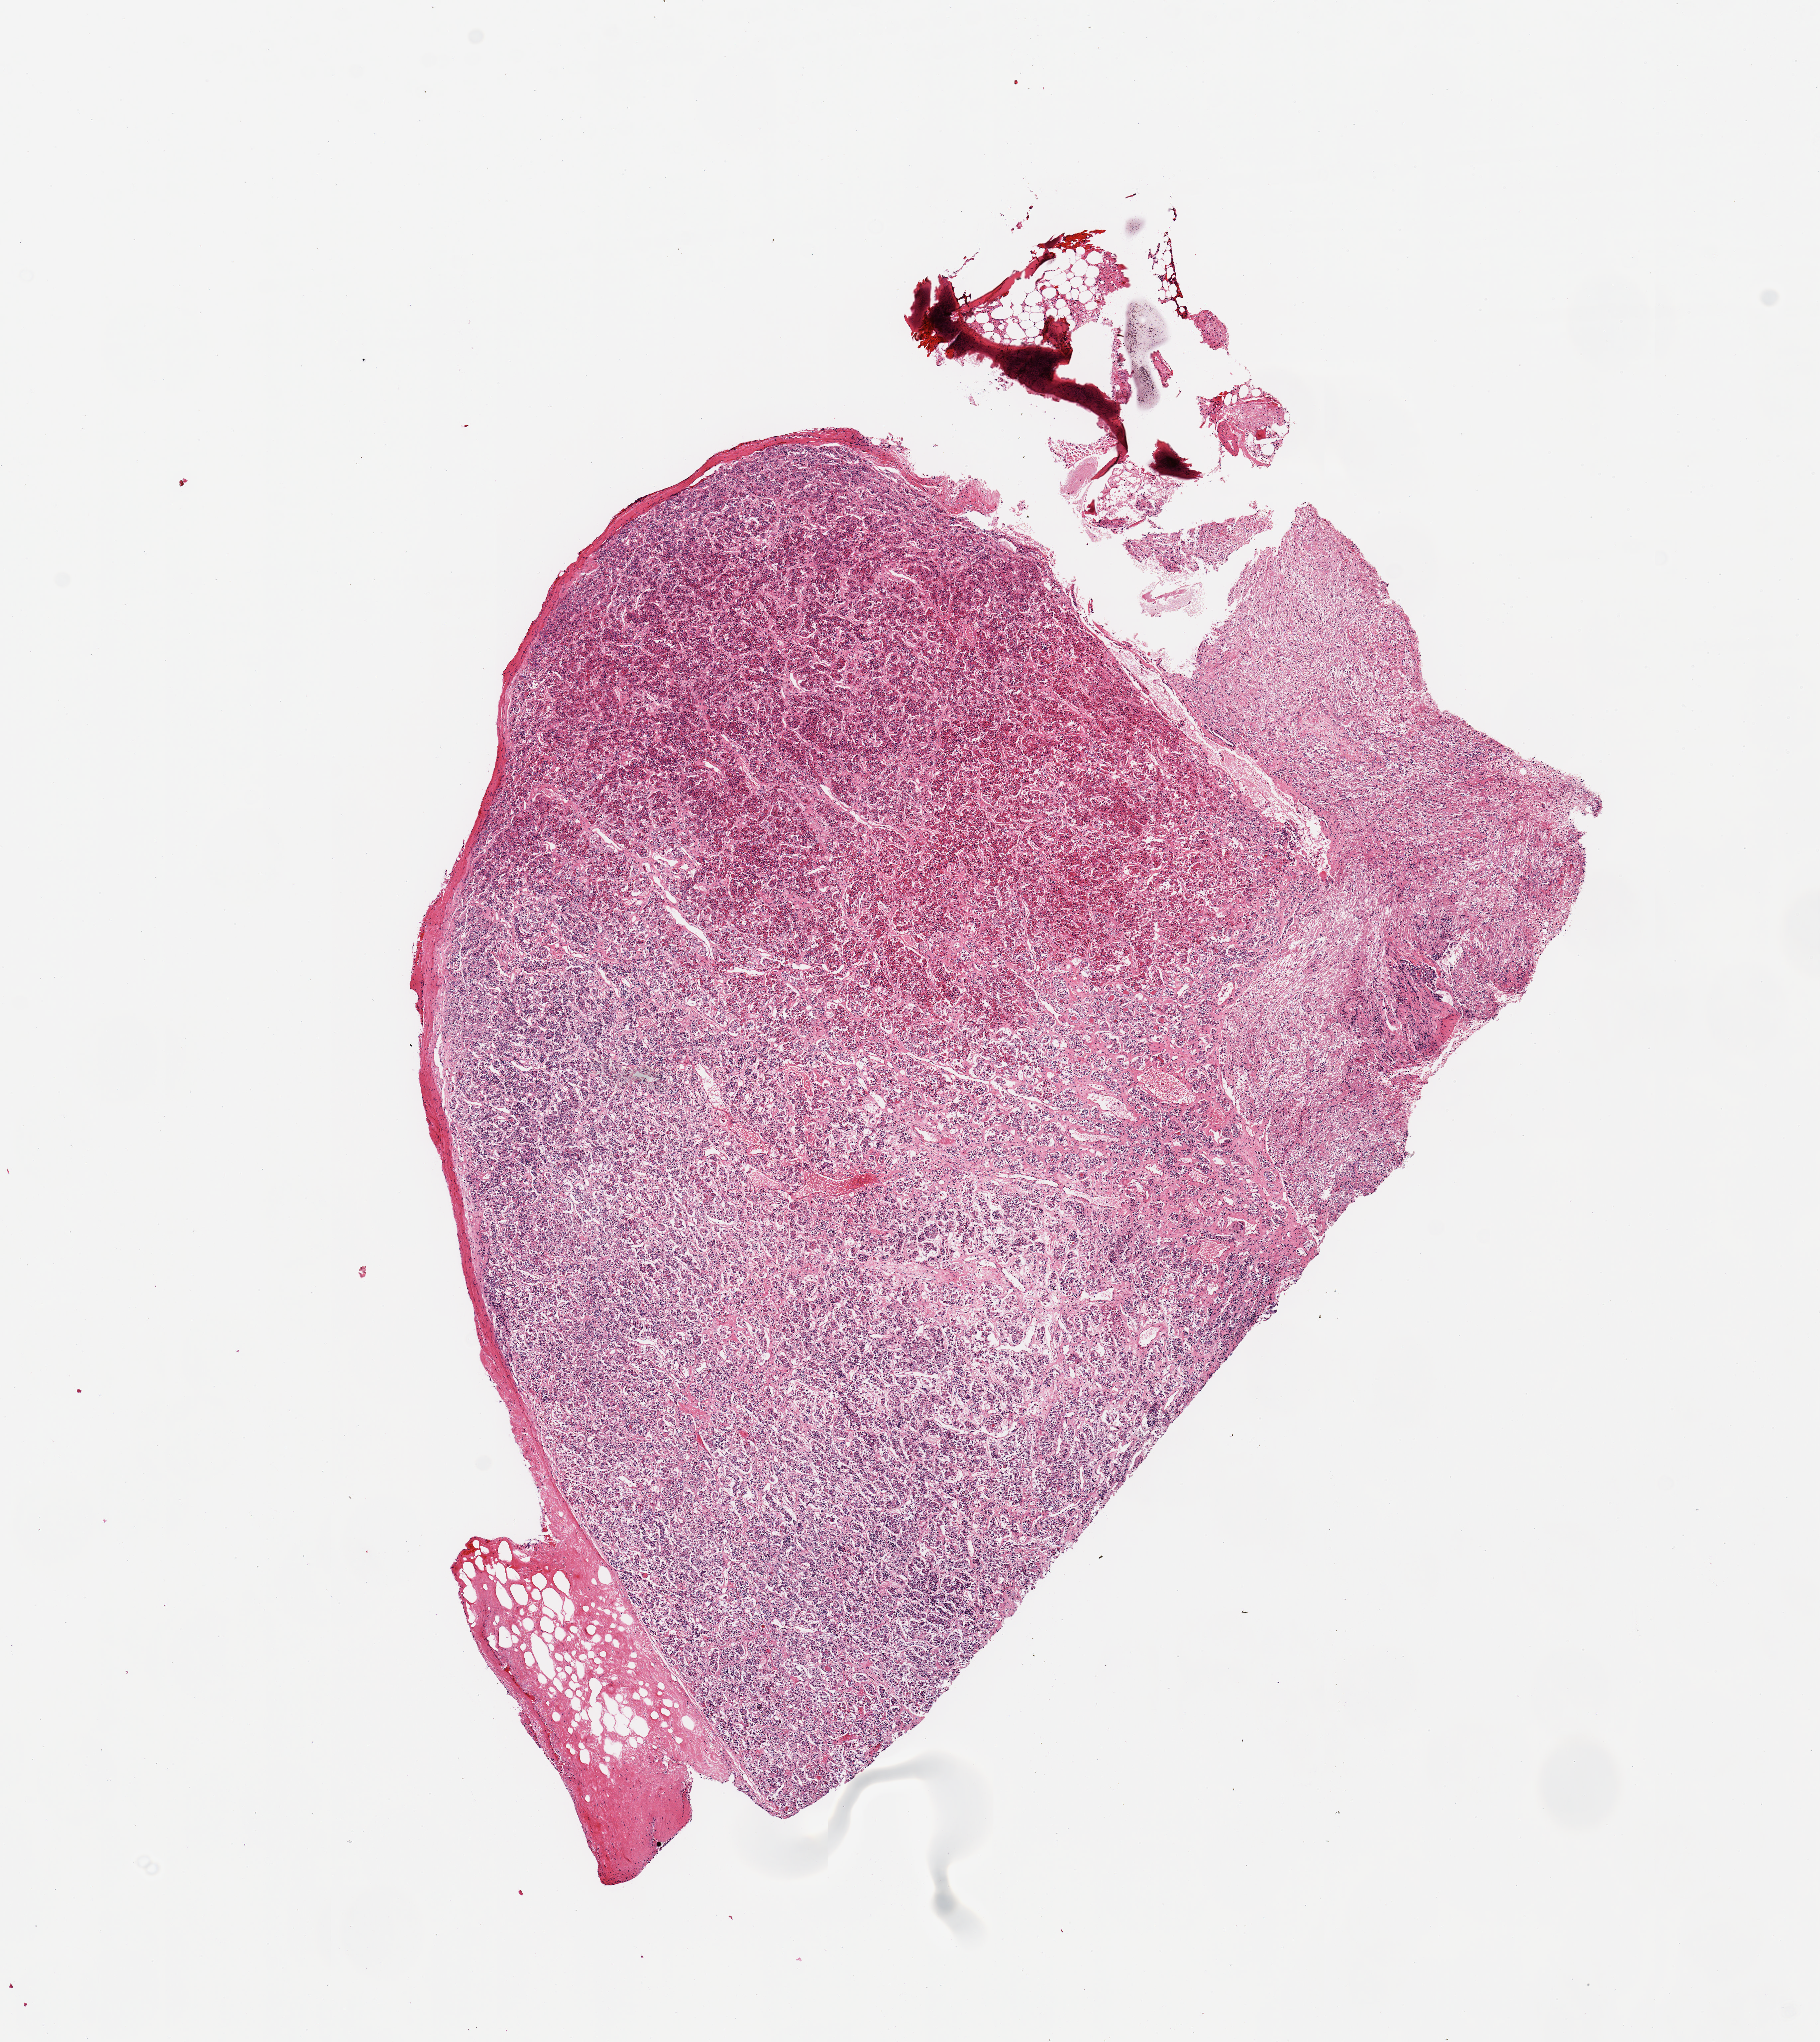
Digitized haematoxylin and eosin-stained section, a low-resolution overview of the entire scanned area, about 10.8 x 12.1 mm (slide scanned at 20x); PAXgene-fixed, paraffin-embedded tissue; sampled site (target tissue): pituitary; tissue donor sample. Male donor.
• review note (as recorded): 1 piece, mainly adenohypophysis; ~4x1.5mm nubbin of neurohypophysis